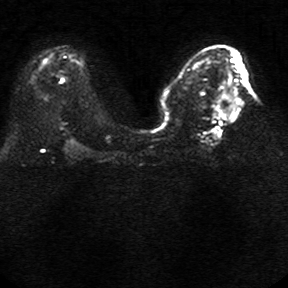
Breast MRI, one axial slice; slice 14 of 34 in the series (ordered by position); diffusion-weighted series; image 2 of 4 stored at this slice position (different b-values; order by instance number); 1.5 T; 5 mm slice thickness; 288 × 288 image matrix, field of view 340 × 340 mm. Female patient.
Outlined on this slice (expert manual segmentation):
- tumour on diffusion-weighted imaging: bounding box (x1, y1, x2, y2) in pixels: (222, 87, 239, 115)